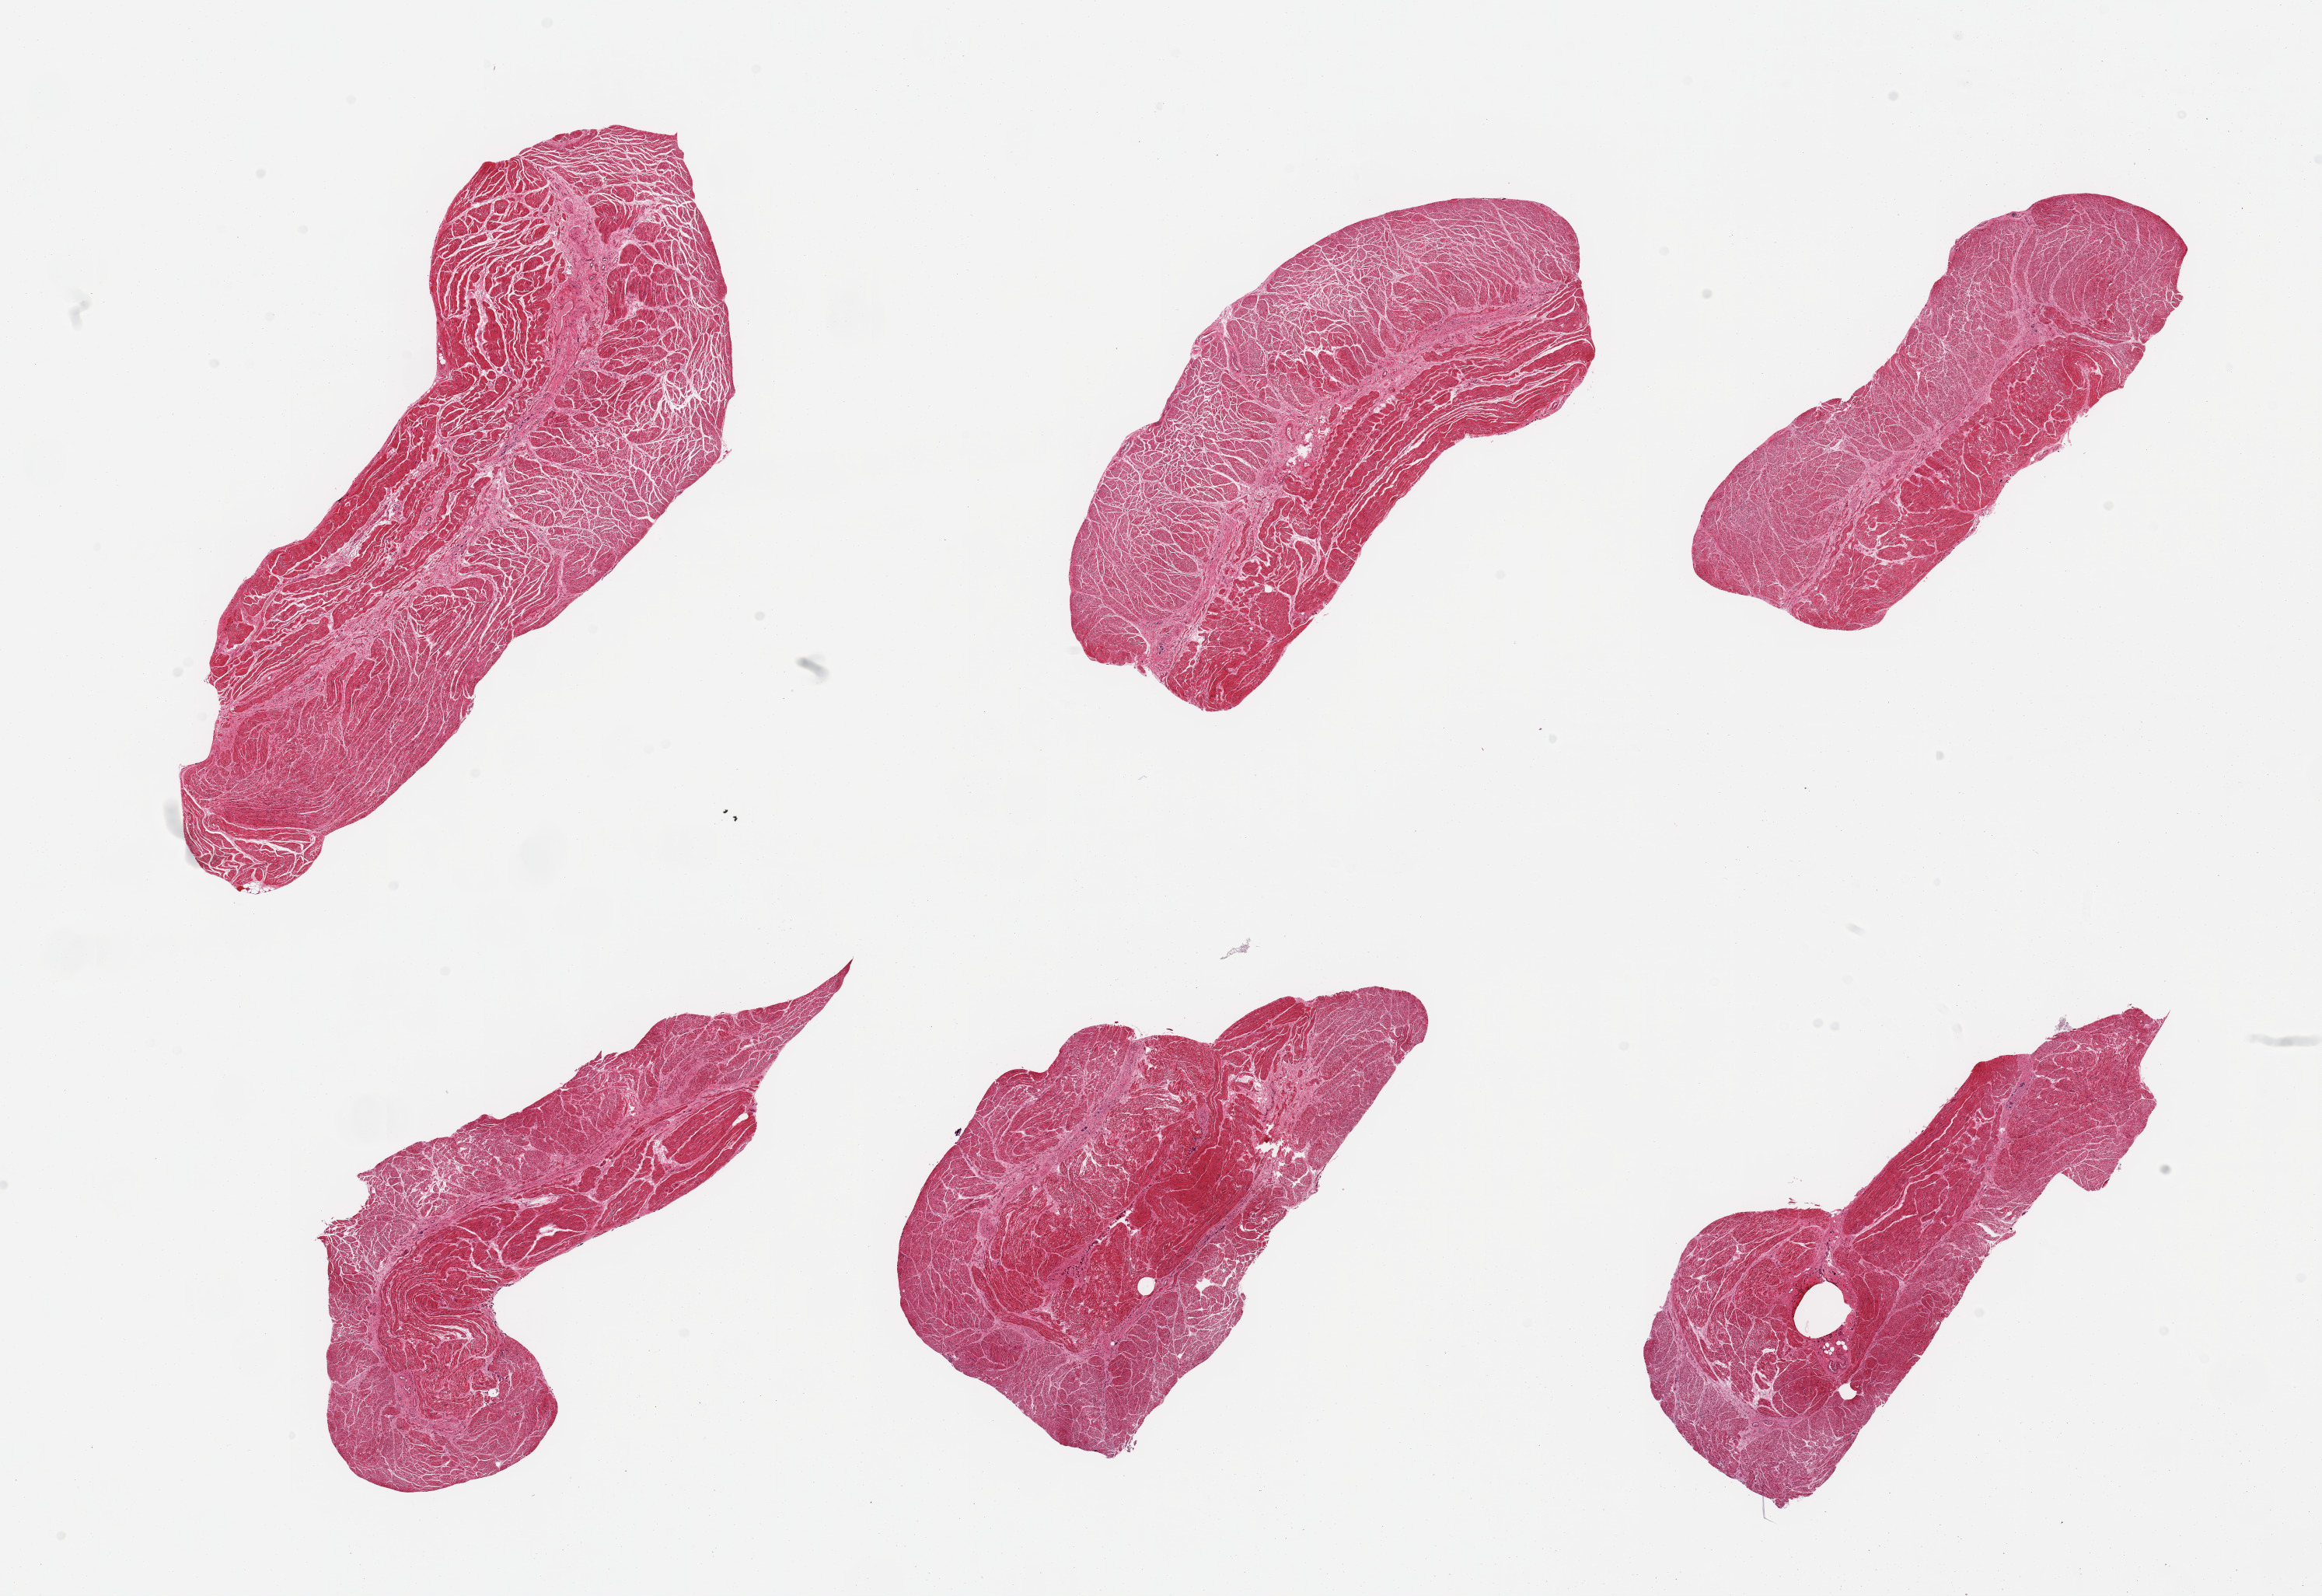
Digitized haematoxylin and eosin-stained section, brightfield — shown as a low-resolution overview of the whole scanned area (about 23.6 x 16.2 mm, acquisition: 20x scan); PAXgene-fixed, paraffin-embedded tissue; section of esophageal muscle (target tissue); tissue donor sample.
Pathologist's review note for this sample: 6 pieces, confirmed target muscularis.